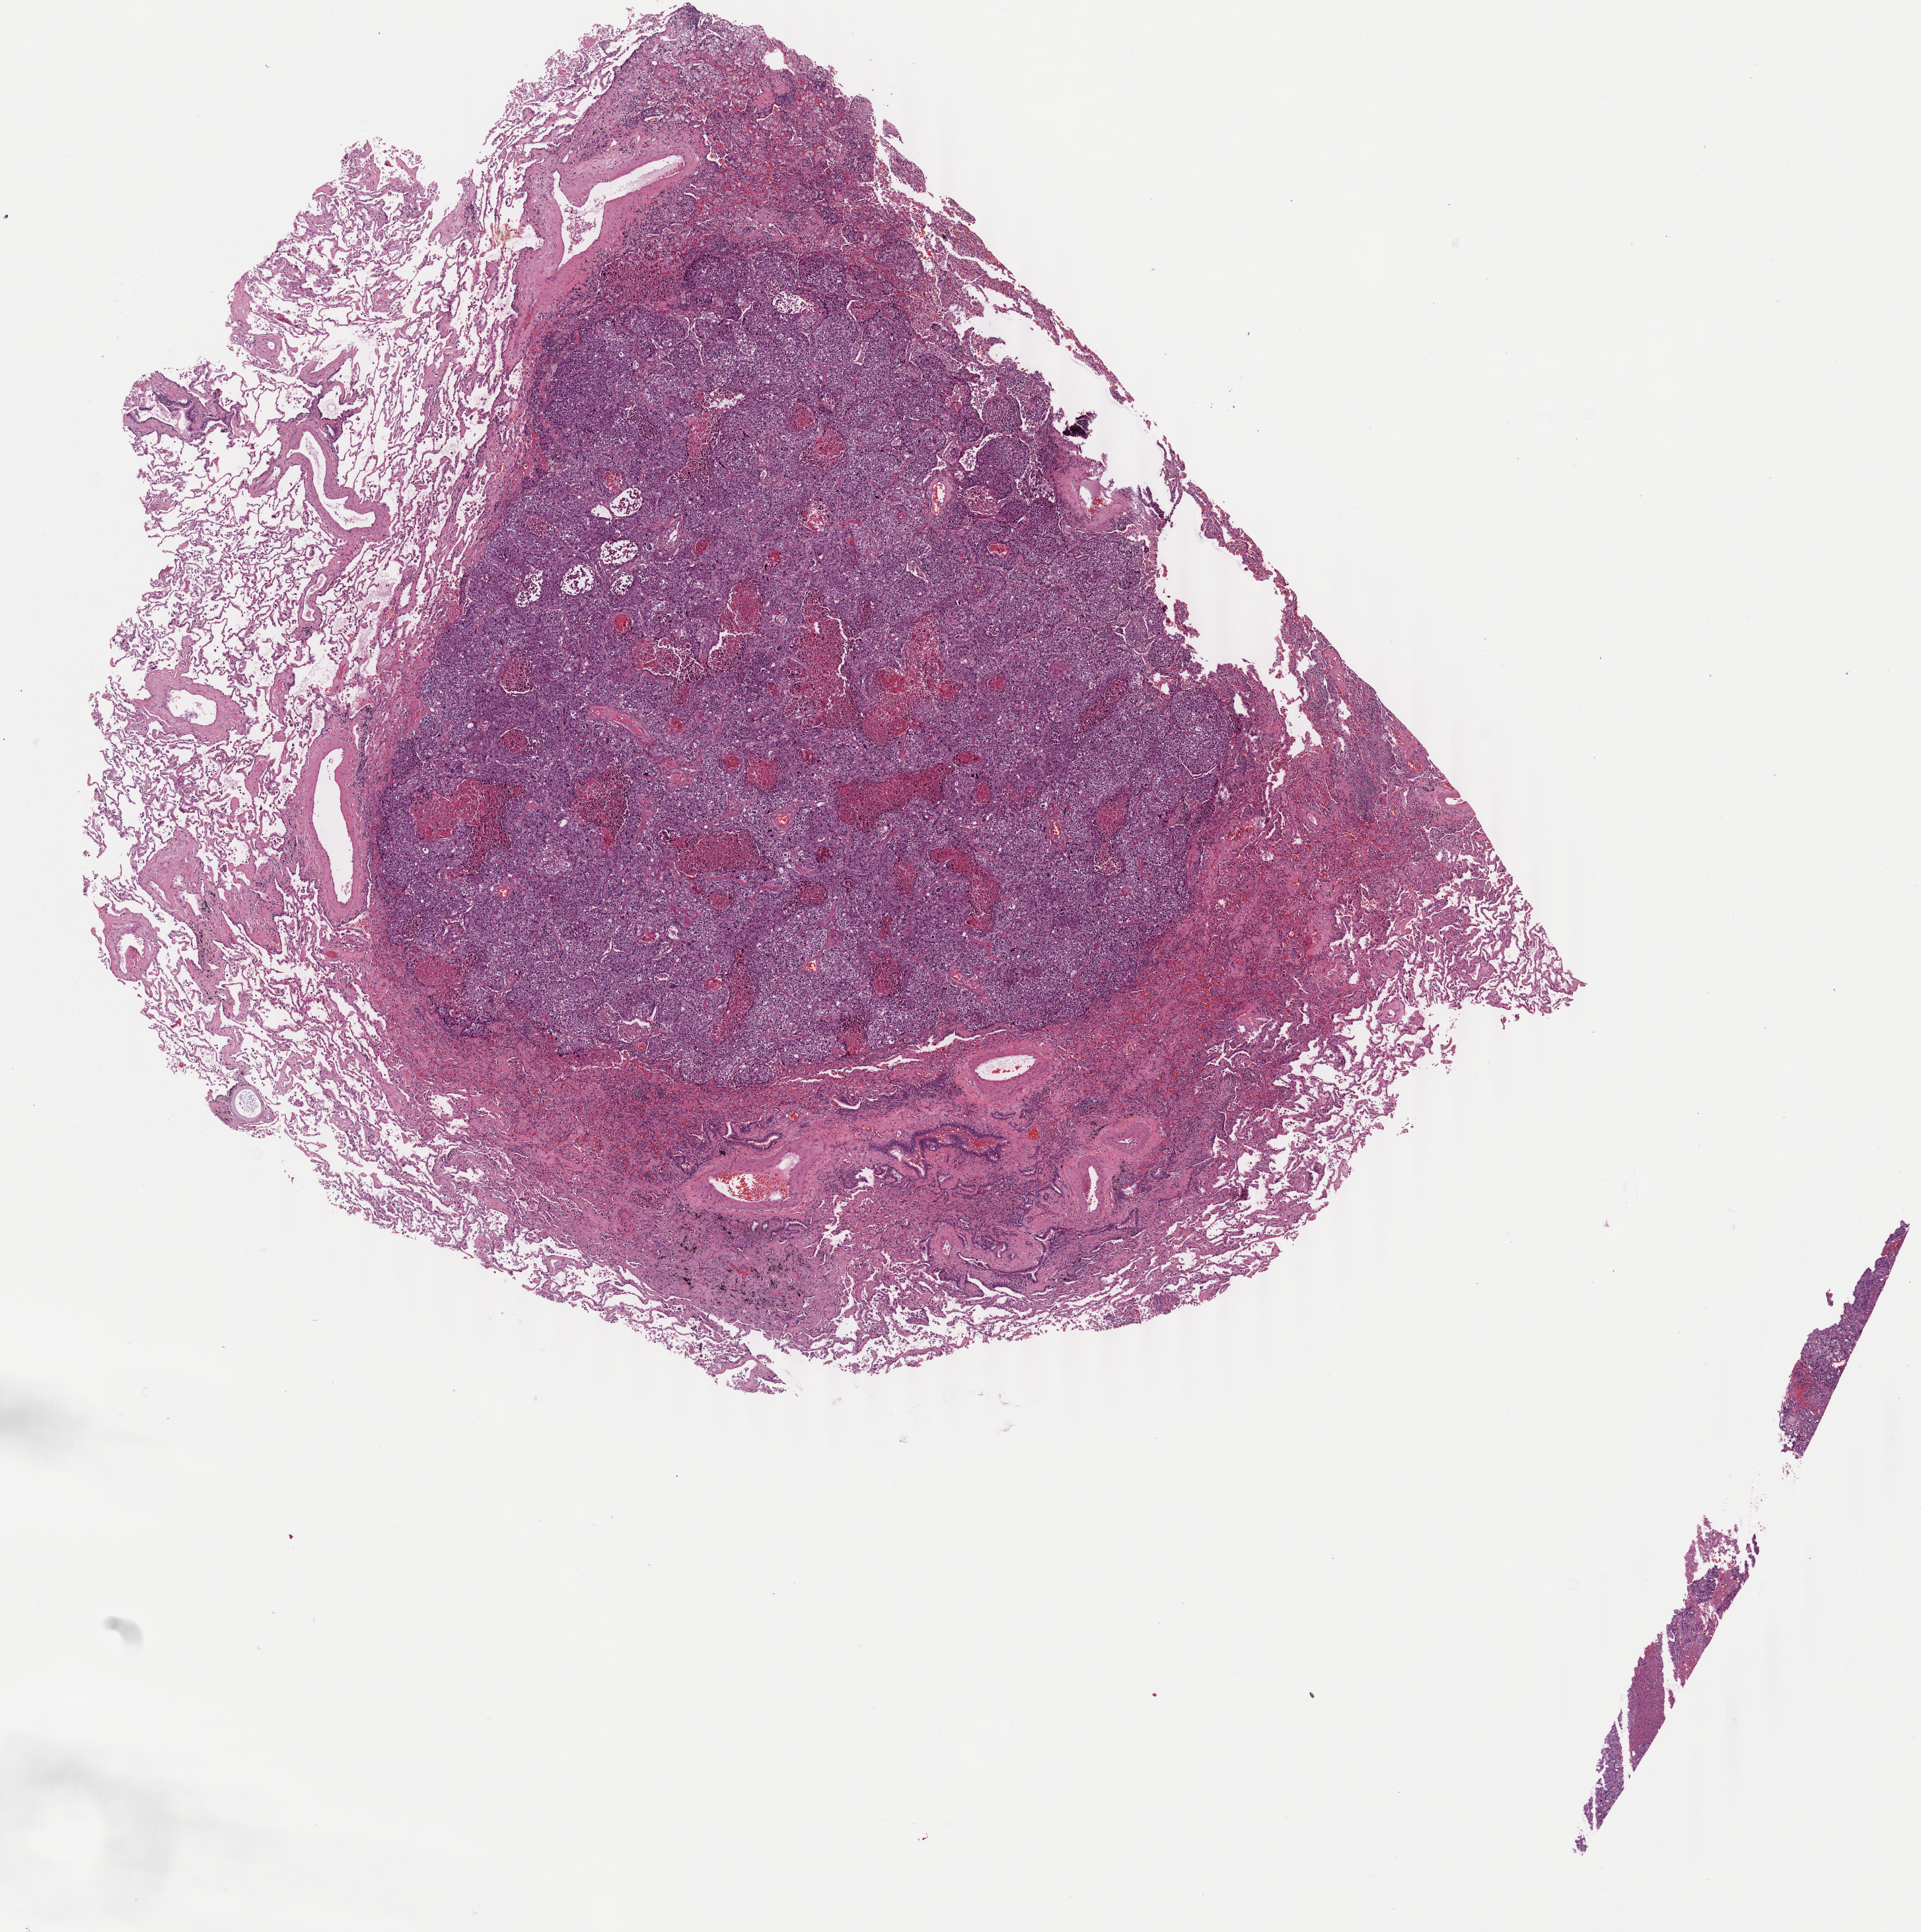
H&E whole-slide image, low-resolution overview of the scanned area, about 11.6 x 11.6 mm, tumor tissue, anatomic site: lung (left). Patient: male, age 66 years.
Diagnosis: Squamous cell carcinoma, NOS.